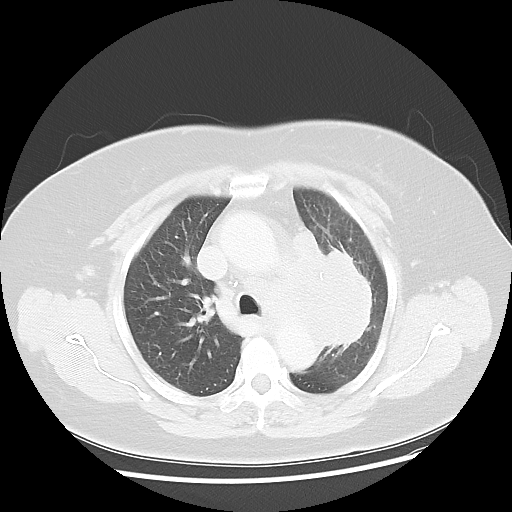
Chest CT, one axial slice; position 33 of 49 along the scan axis; 120 kVp; lung window (W 1500 / L -600 HU); 5 mm slice thickness; 512 × 512 image matrix, field of view 374 × 374 mm. Patient: female, 58 years. From the clinical record (not read from this slice): clinical TNM (as recorded): T4 N3 M0; histopathological grade: G3.
Structures marked on this image (bounding box drawn by a radiologist):
- lung tumour (recorded histology: small cell carcinoma): box from (x=275, y=223) to (x=386, y=368) px